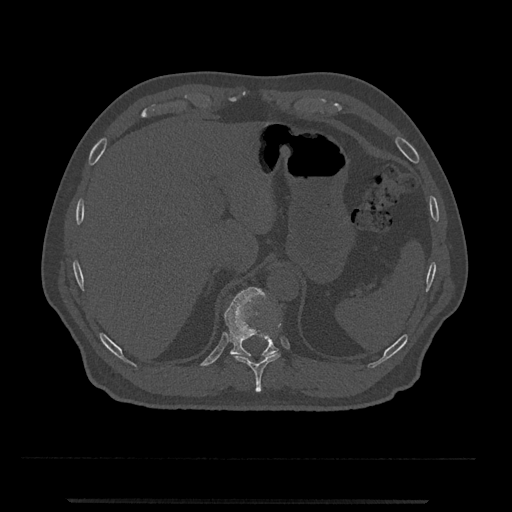
CT including the spine, one axial slice; position 492 of 797 along the scan axis; reconstruction kernel Br40s/3; bone window (W 1800 / L 400 HU); 0.5 mm slice thickness; 512 × 512 image matrix. Patient: male, 63 years. Case-level facts recorded for this patient, not image findings: primary cancer: prostate.
Outlined on this slice (semi-automatically segmented with operator editing):
- T10 vertebra: bounding box <234,323,281,393> (left, top, right, bottom; pixels)
- T11 vertebra: <224,287,278,357>